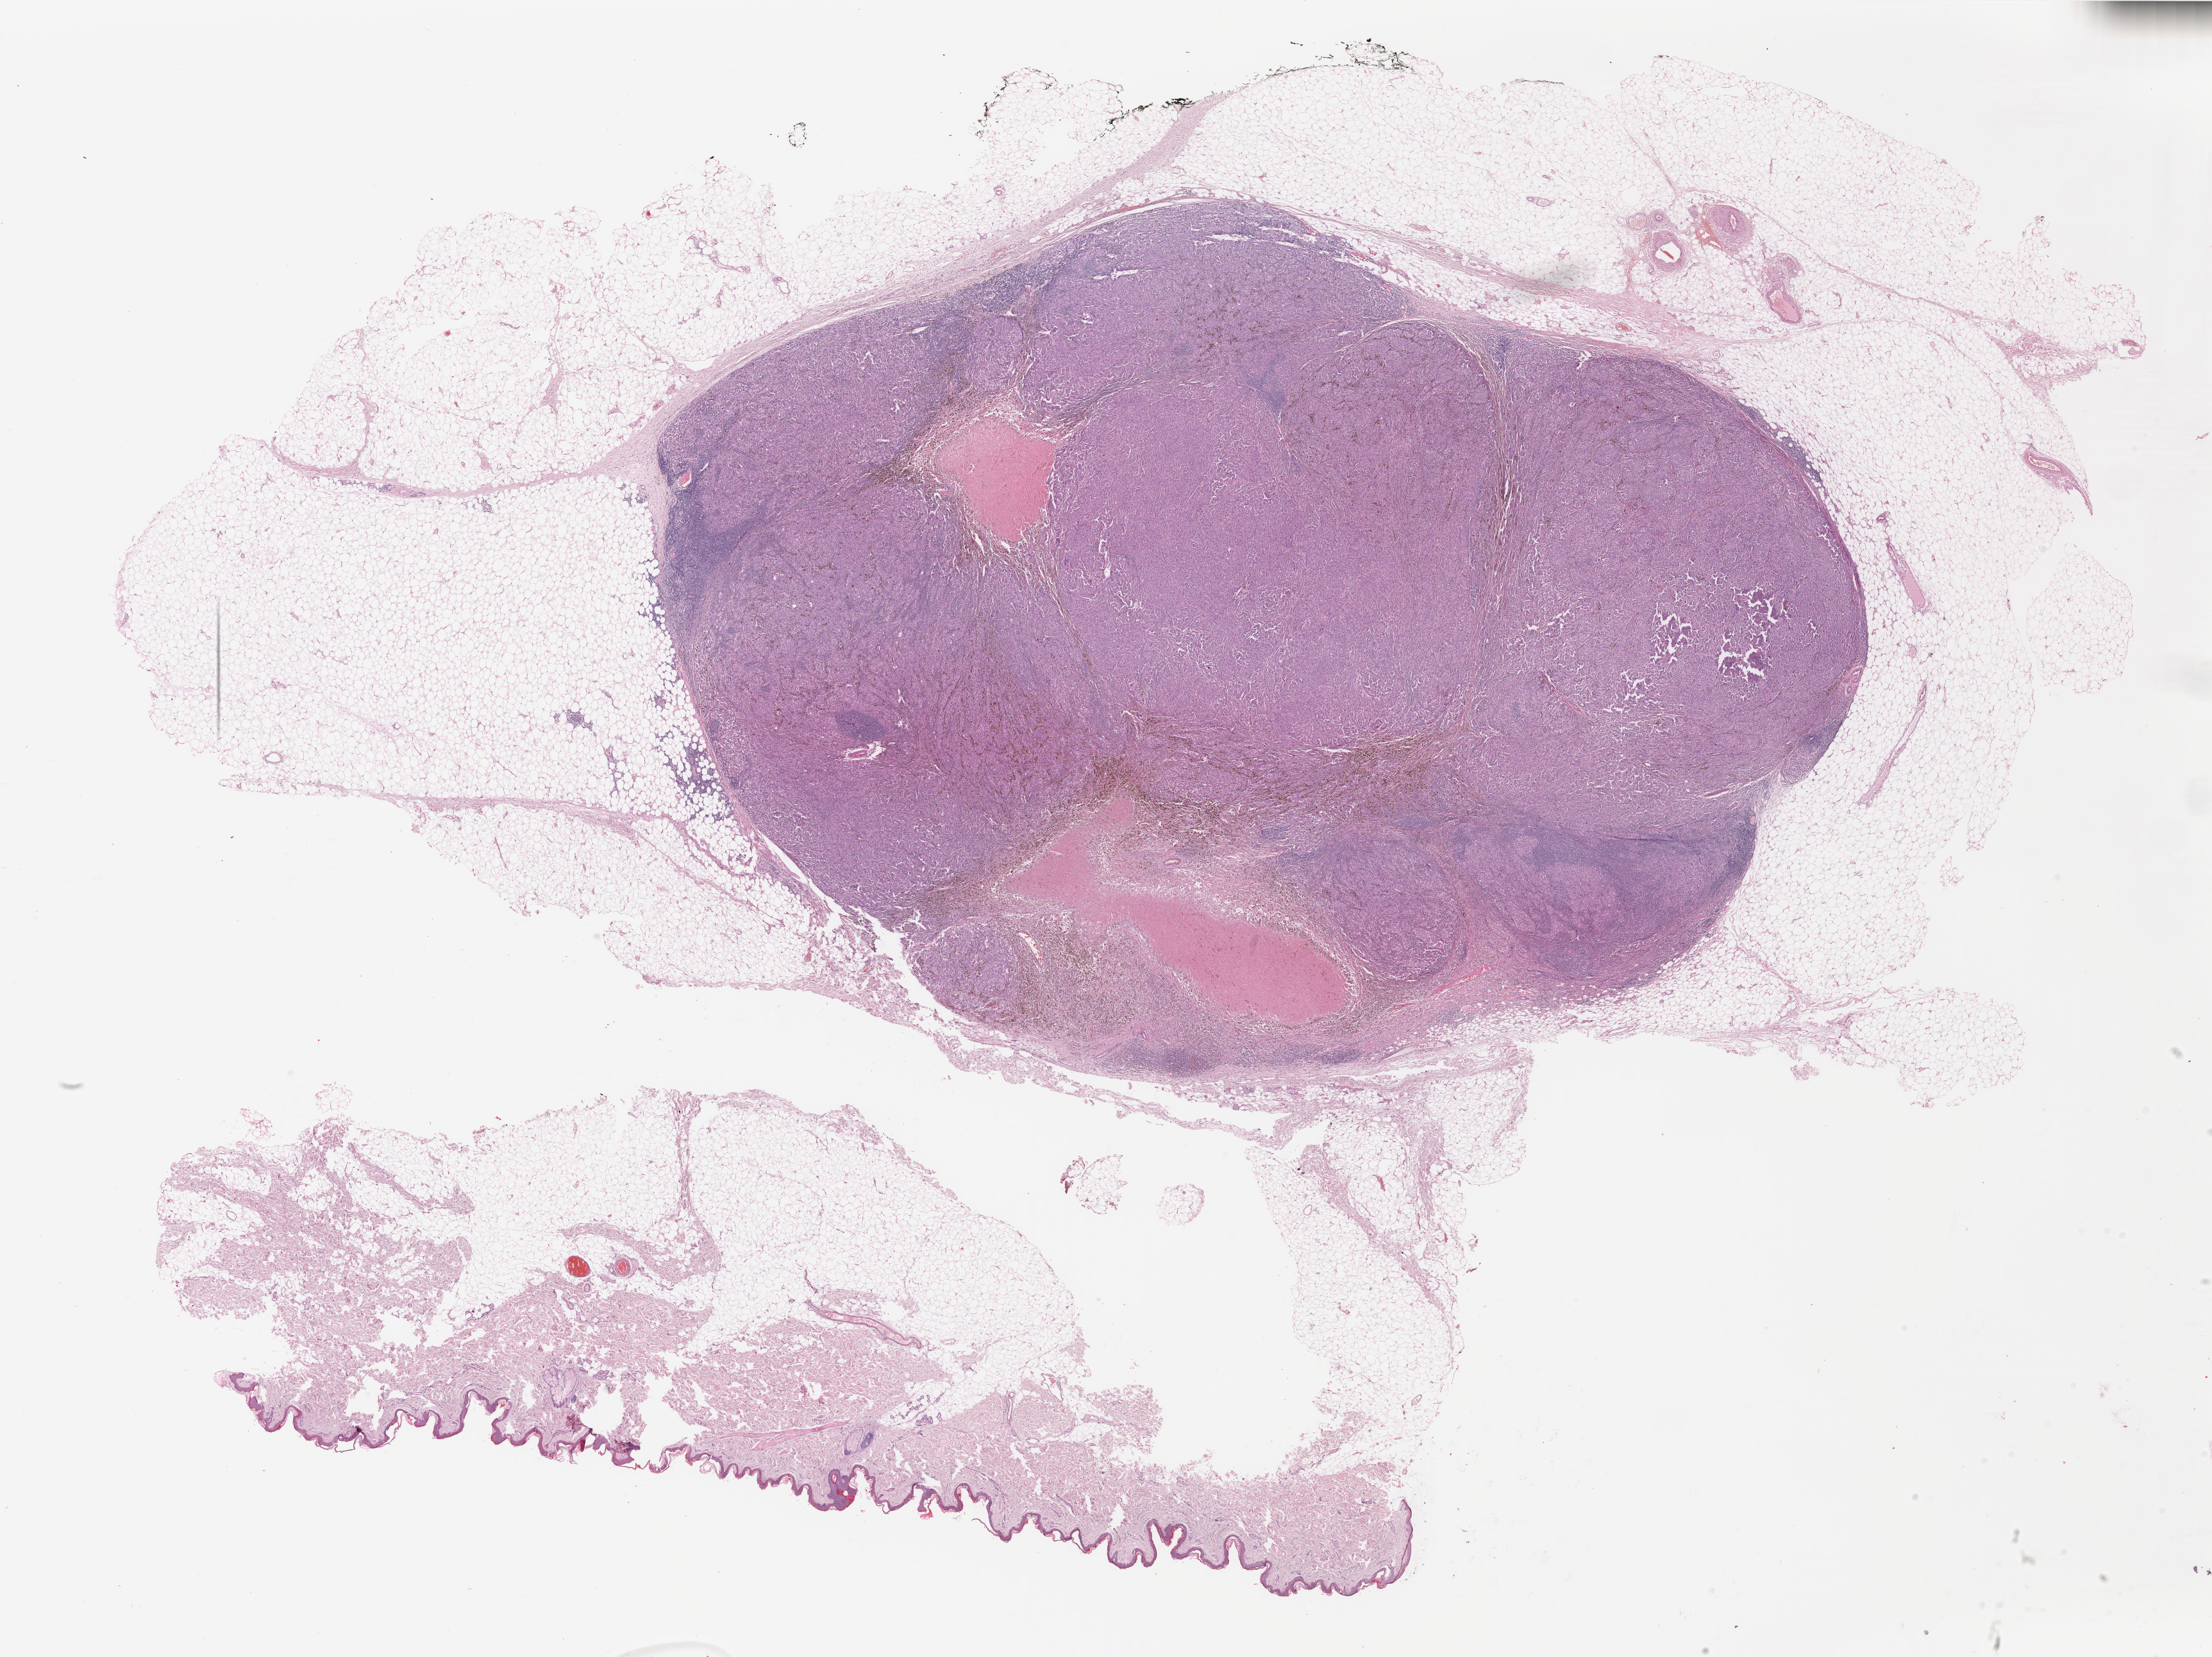
Digitized Hematoxylin and eosin (H&E) stained tissue section (whole slide) — shown as a low-resolution overview of the whole scanned area (about 27.4 x 20.5 mm, acquisition: 40x scan); formalin-fixed paraffin-embedded (FFPE) diagnostic section; primary tumour sample from the skin. Patient: female, age at initial diagnosis 65 years.
Diagnosis: Malignant melanoma, NOS.